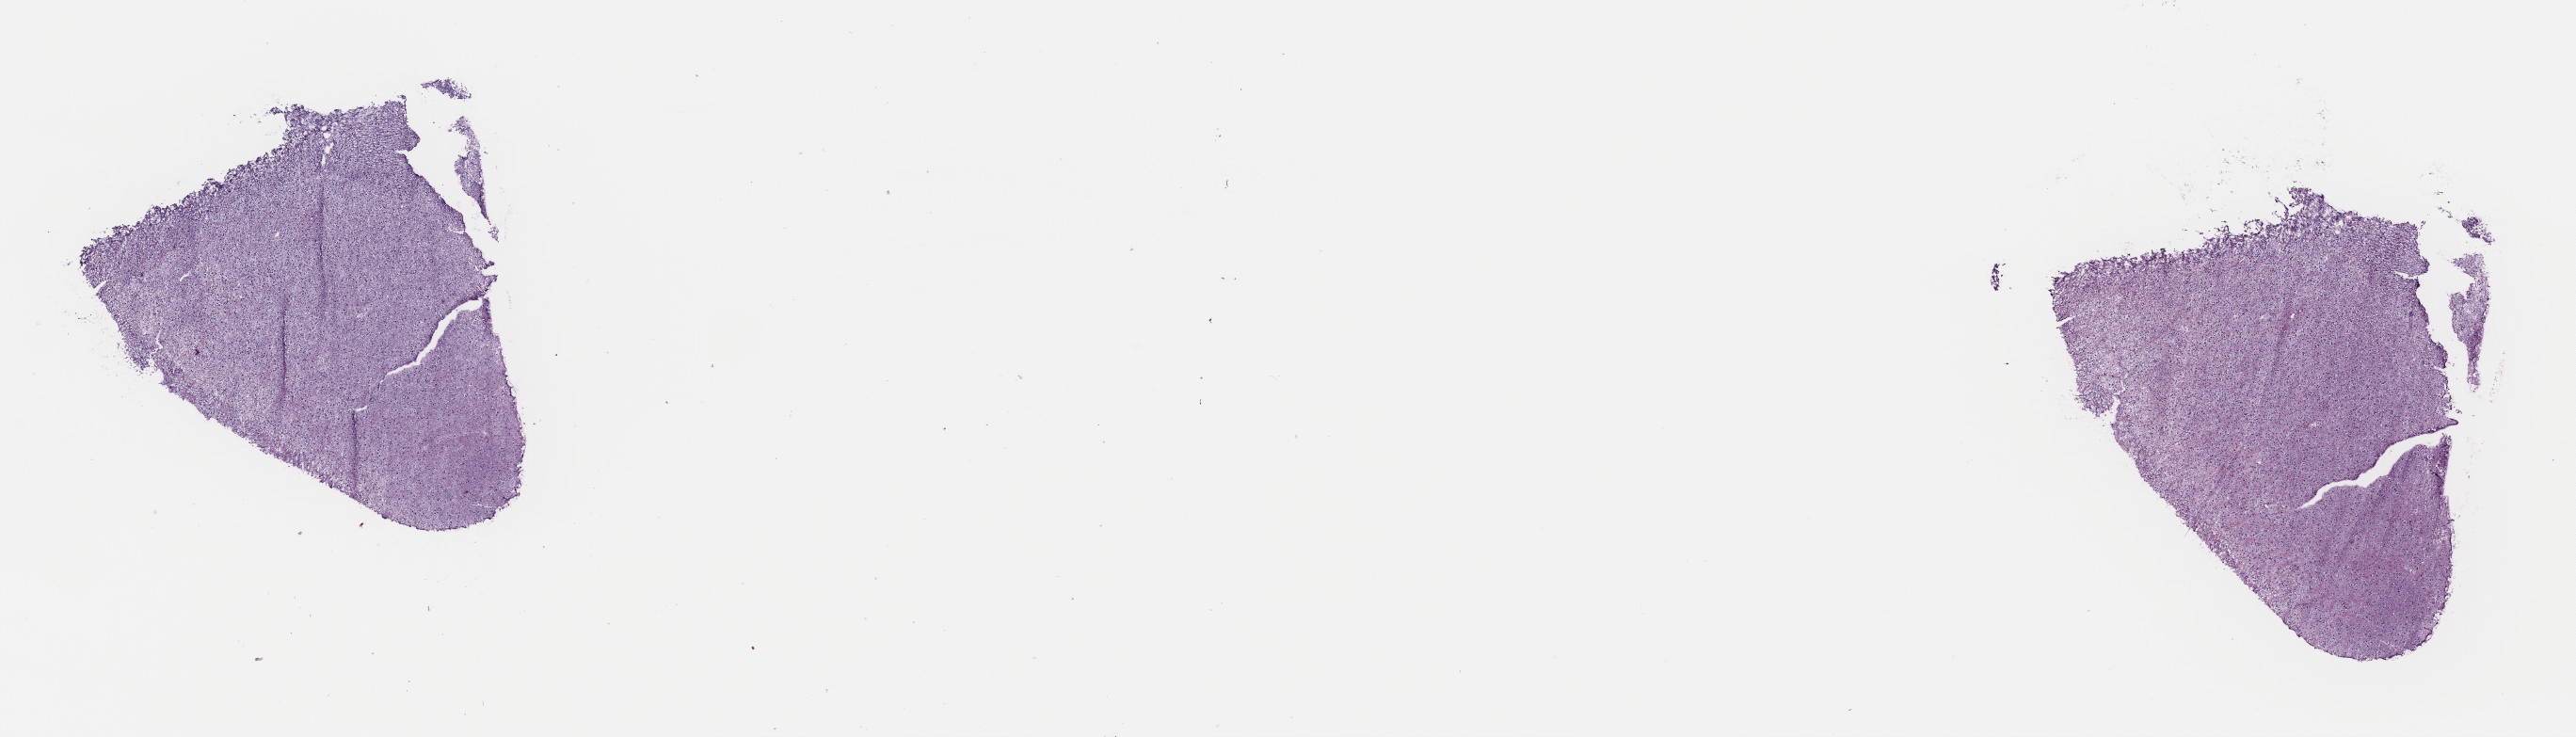
Whole-slide histology image, H&E — a low-resolution overview of the entire scanned area, about 21.6 x 6.2 mm; frozen section from the top of the tissue portion; brain, primary tumour sample. Female patient; age at initial diagnosis 57 years. Histologic grade: G2 (moderately differentiated). Composition of this section per pathologist review: tumour cells 40%, tumour nuclei 80%, normal cells 10%, stromal cells 50%, necrosis 0%. Infiltration values recorded for this section: lymphocyte infiltration 0%, monocyte infiltration 0%, neutrophil infiltration 0%.
* diagnosis: Mixed glioma (cerebrum)